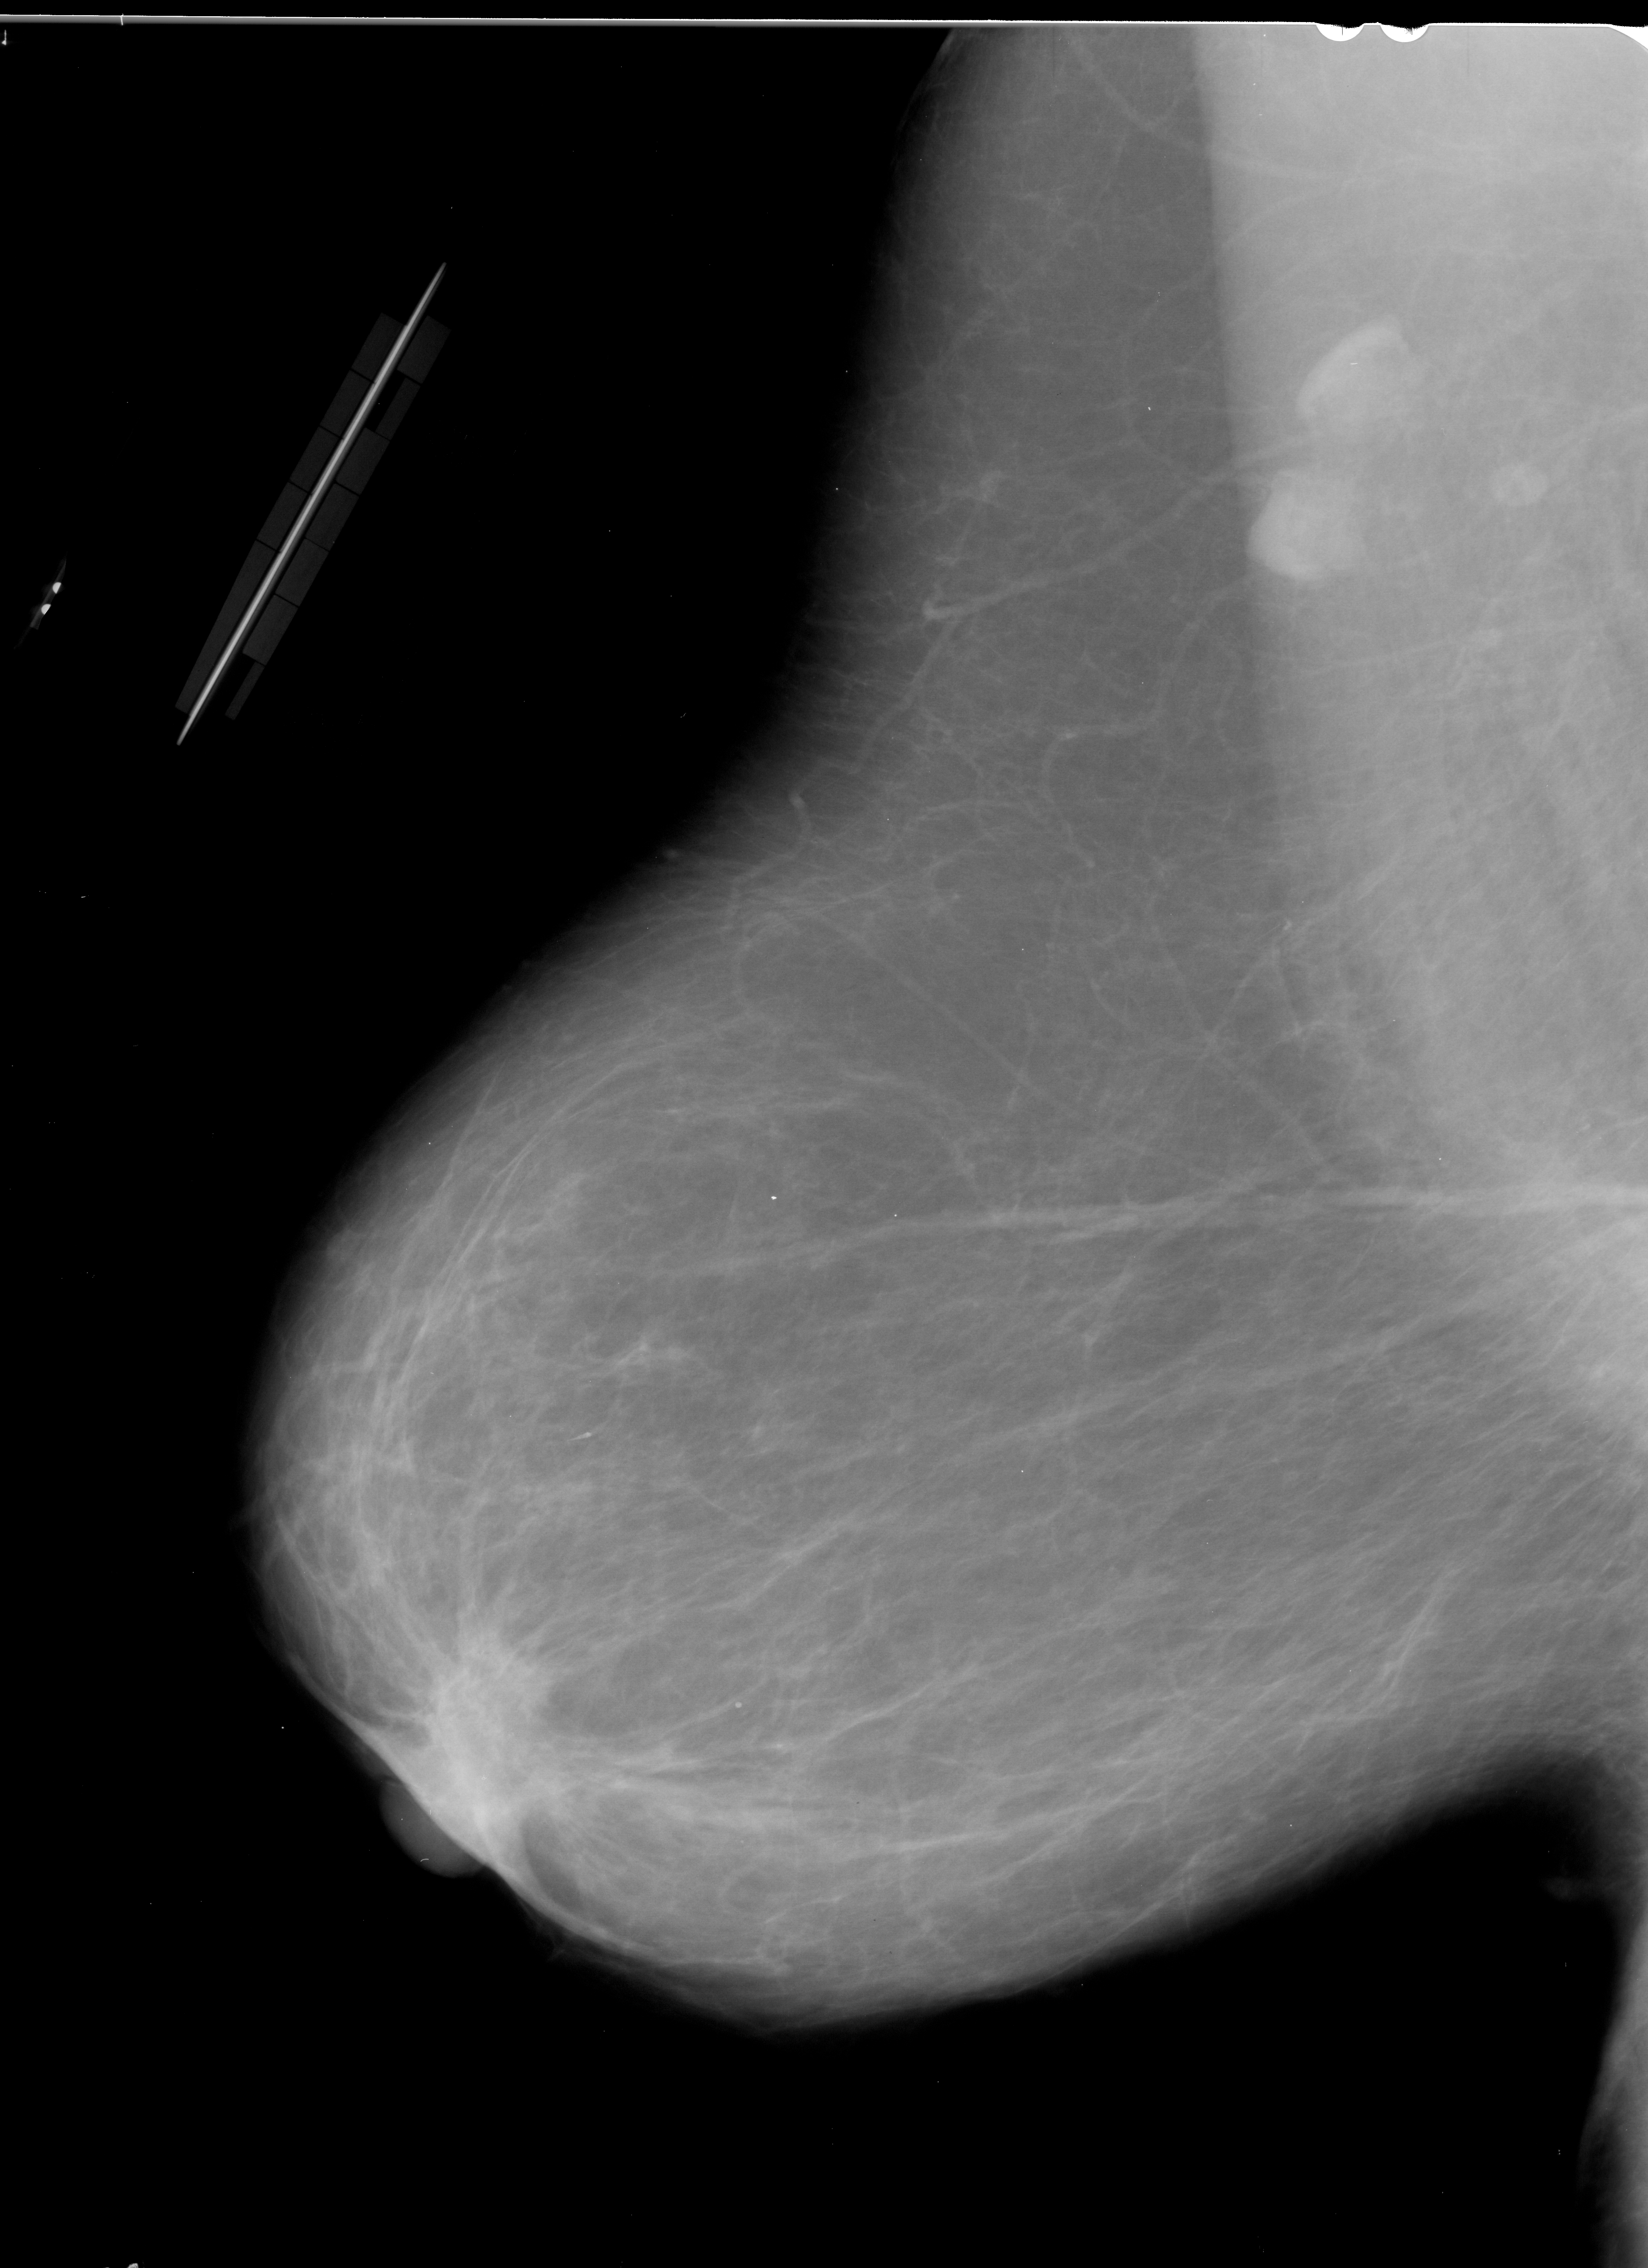
Mammogram (digitized film), left breast, MLO view, breast composition: scattered fibroglandular densities (BI-RADS density category 2 of 4).
Mass, shape irregular, margins spiculated; BI-RADS assessment category 5; subtlety rating 4 on a 1 (subtle) to 5 (obvious) scale; pathology (as recorded): malignant.